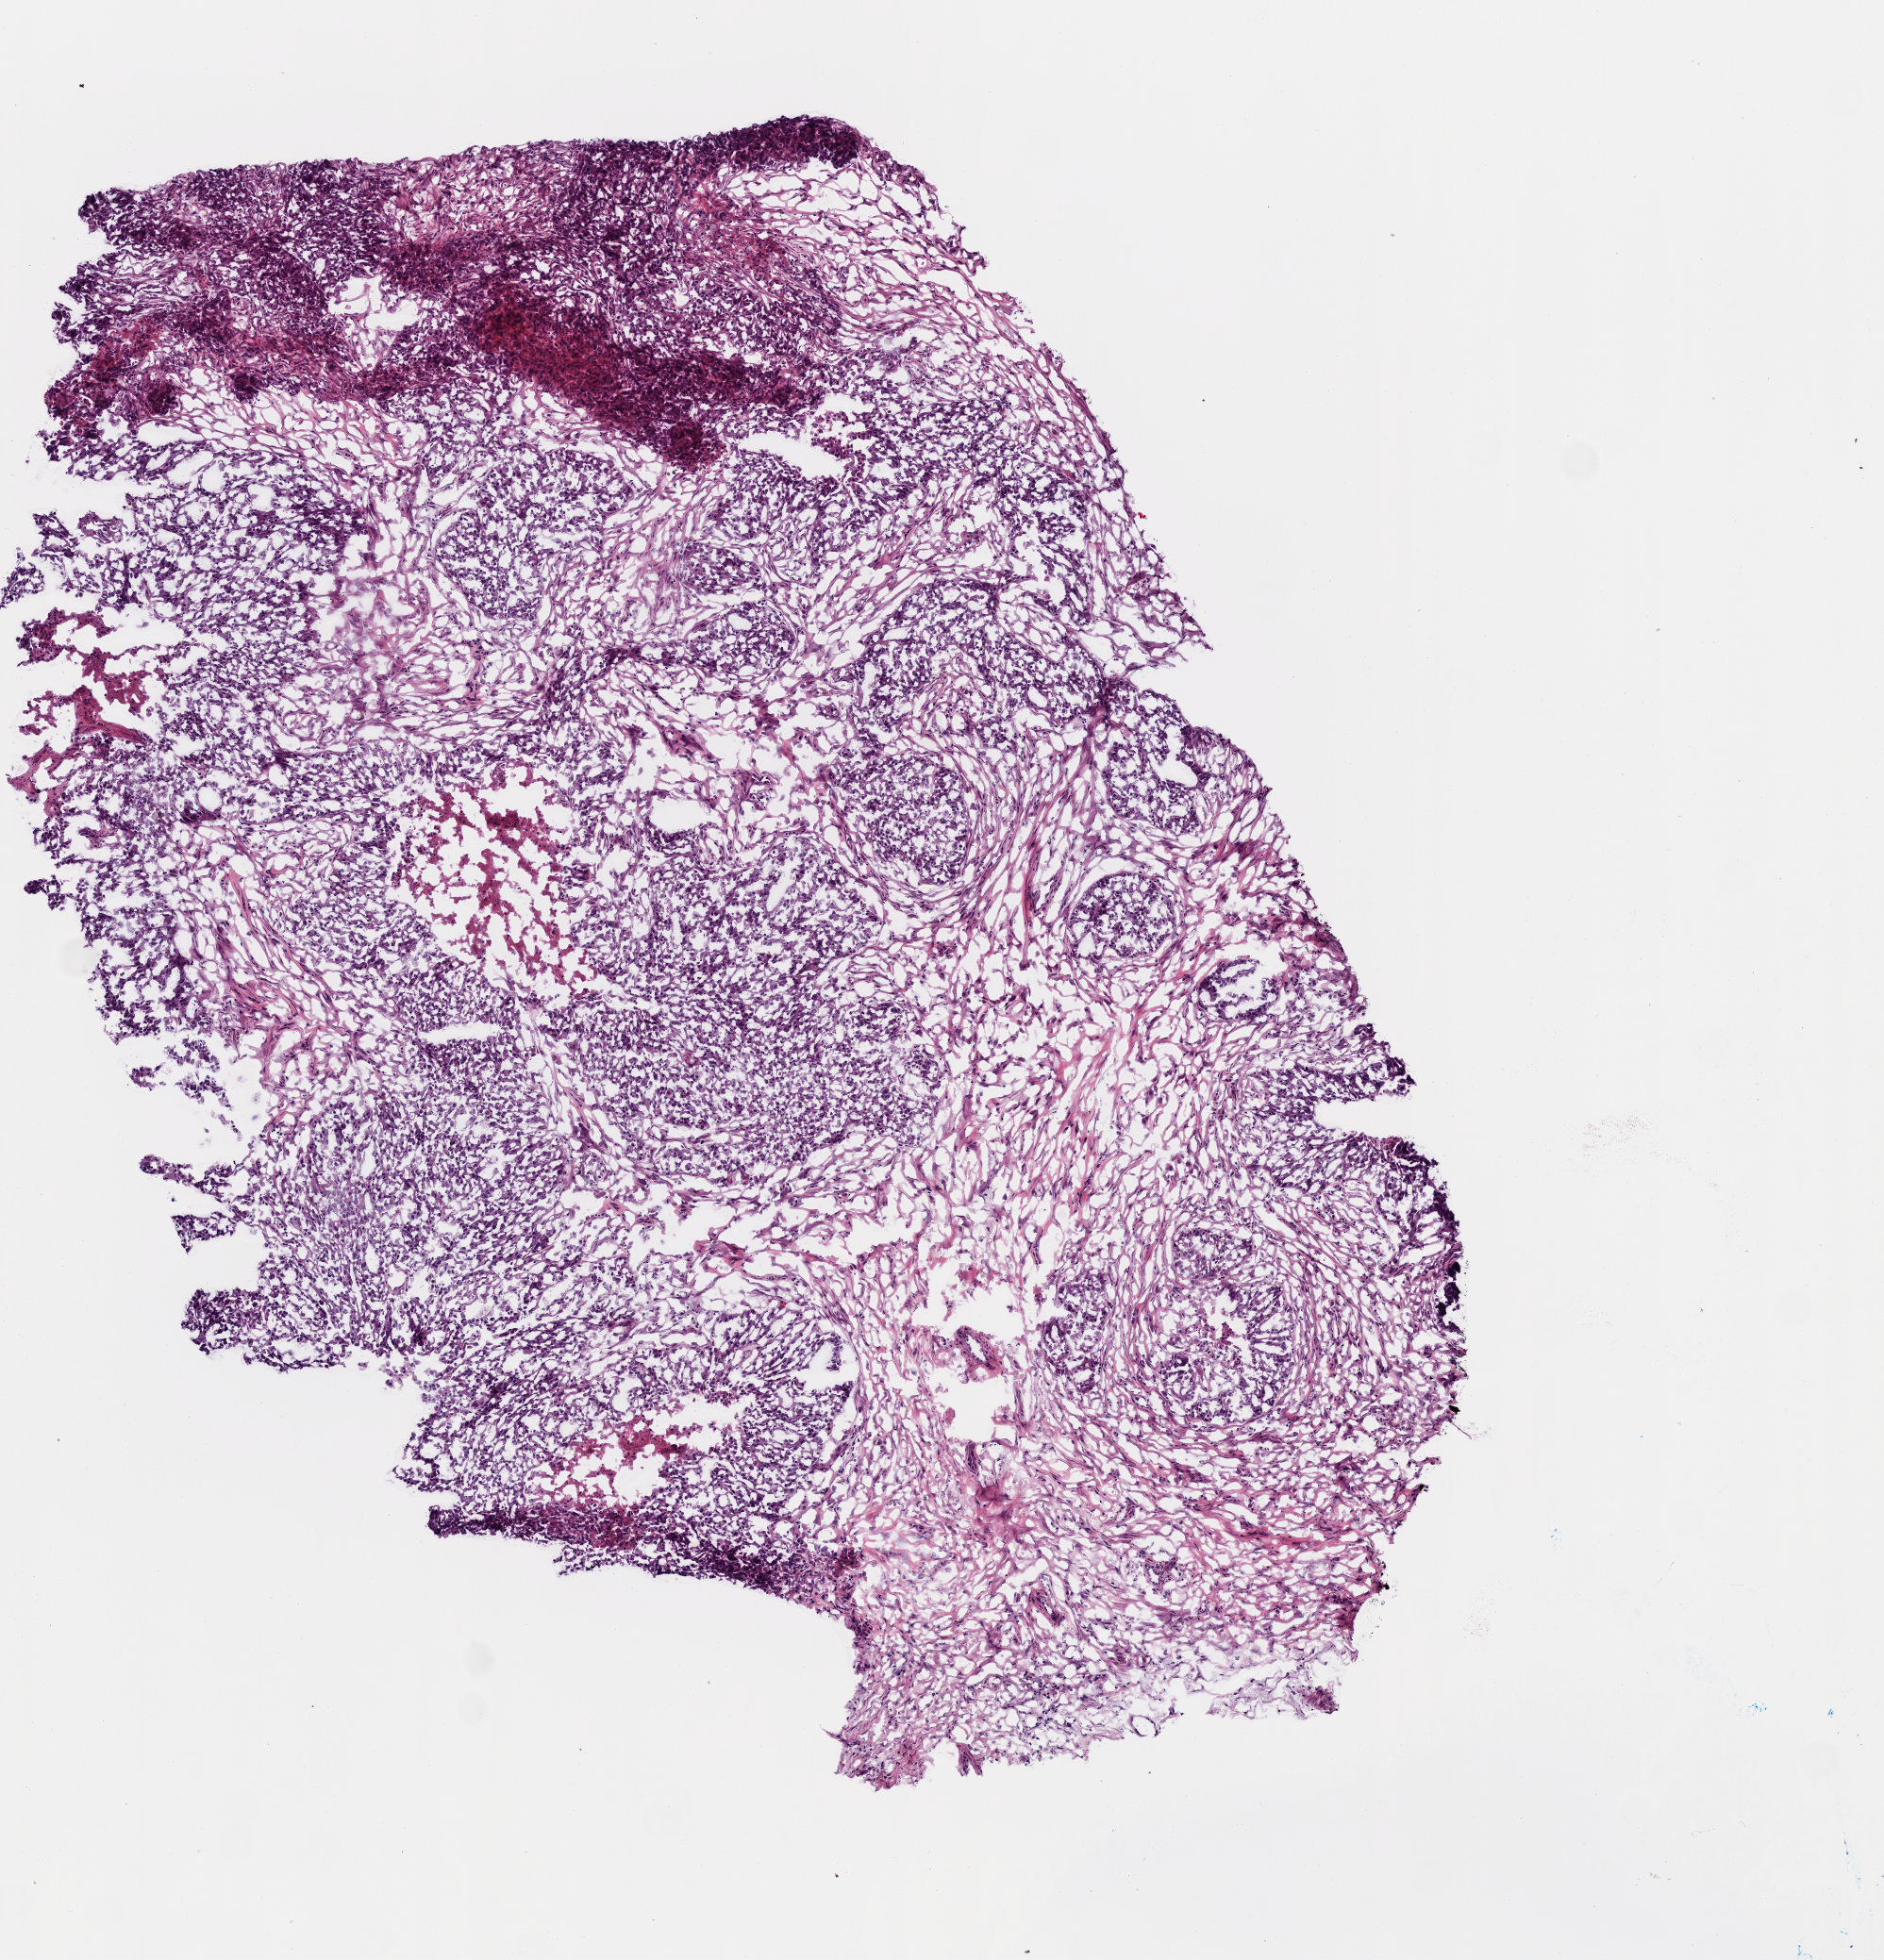
Whole-slide histology image, H&E-stained — low-resolution overview of the scanned area, about 4.0 x 4.2 mm (acquisition: 20x scan). Frozen section from the top of the tissue portion. Sample: primary tumour, ovary. Patient: female, age at initial diagnosis 45 years.
Pathologic diagnosis: Serous cystadenocarcinoma, NOS.